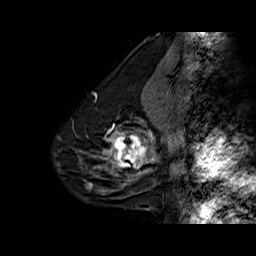
Breast MRI (dynamic contrast-enhanced), one sagittal slice; position 18 of 60 along the scan axis; dynamic contrast-enhanced series, time point 2 of 6 at this slice position (early post-contrast); 1.5 T; TE 6.3 ms, TR 32.5 ms; 256 × 256 image matrix, field of view 200 × 200 mm. Female patient. From the clinical record (not read from this slice): setting: breast cancer imaged before/during neoadjuvant chemotherapy; receptor status: triple-negative.
Annotated regions visible in this slice (semi-automatically segmented with operator editing):
- analysis volume of interest (the breast-tissue region the enhancement analysis was run in; not a lesion): bounding box [x1, y1, x2, y2] px = [108, 126, 154, 177]
- tumour enhancement mask (voxels above the 100 % enhancement threshold inside the analysis volume of interest): [108, 132, 154, 168]